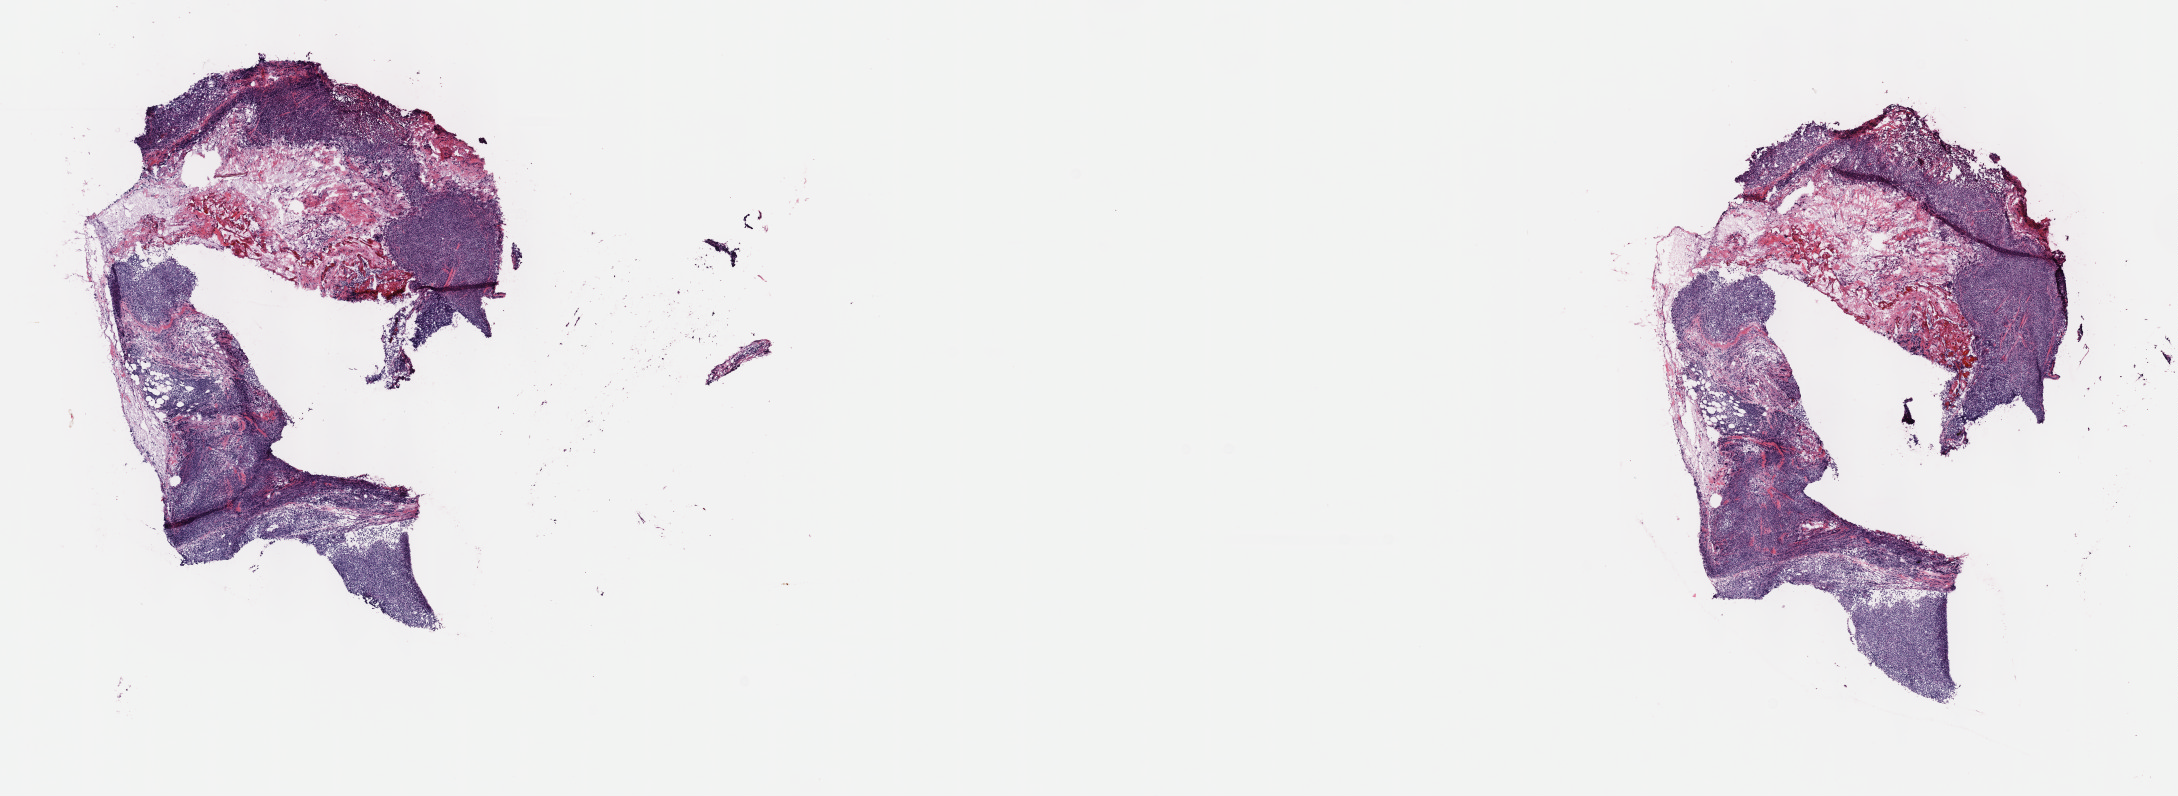
Hematoxylin and eosin (H&E) stained whole-slide image — low-resolution overview of the scanned area, about 17.6 x 6.4 mm (acquisition: 40x scan), frozen section from the top of the tissue portion, lymphoid tissue, primary tumour sample. Patient: male, age at initial diagnosis 61 years. Pathologist review of this section (percent, as recorded): tumour cells 50%, tumour nuclei 60%, normal cells 10%, stromal cells 35%, necrosis 5%. Infiltration values recorded for this section: lymphocyte infiltration 80%, monocyte infiltration 10%, neutrophil infiltration 0%.
Pathologic diagnosis: Diffuse large B-cell lymphoma, NOS (lymph nodes of head, face and neck).